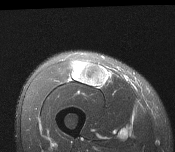
MRI of an extremity soft-tissue mass, one axial slice; slice 53 of 116 in the series (ordered by position); T2-weighted fat-saturated; MR volume resampled by the dataset authors to the PET/CT grid (not the native acquisition matrix); 175 × 152 image matrix, field of view 171 × 148 mm. Male patient. From the clinical record (not read from this slice): histological type: pleiomorphic leiomyosarcoma; grade: intermediate; site of the primary tumour: right thigh.
Outlined on this slice (expert contour drawn on MRI and transferred to this co-registered scan by the dataset authors):
- gross tumour volume including surrounding oedema: bounding box (x1, y1, x2, y2) in pixels: (72, 61, 109, 89)